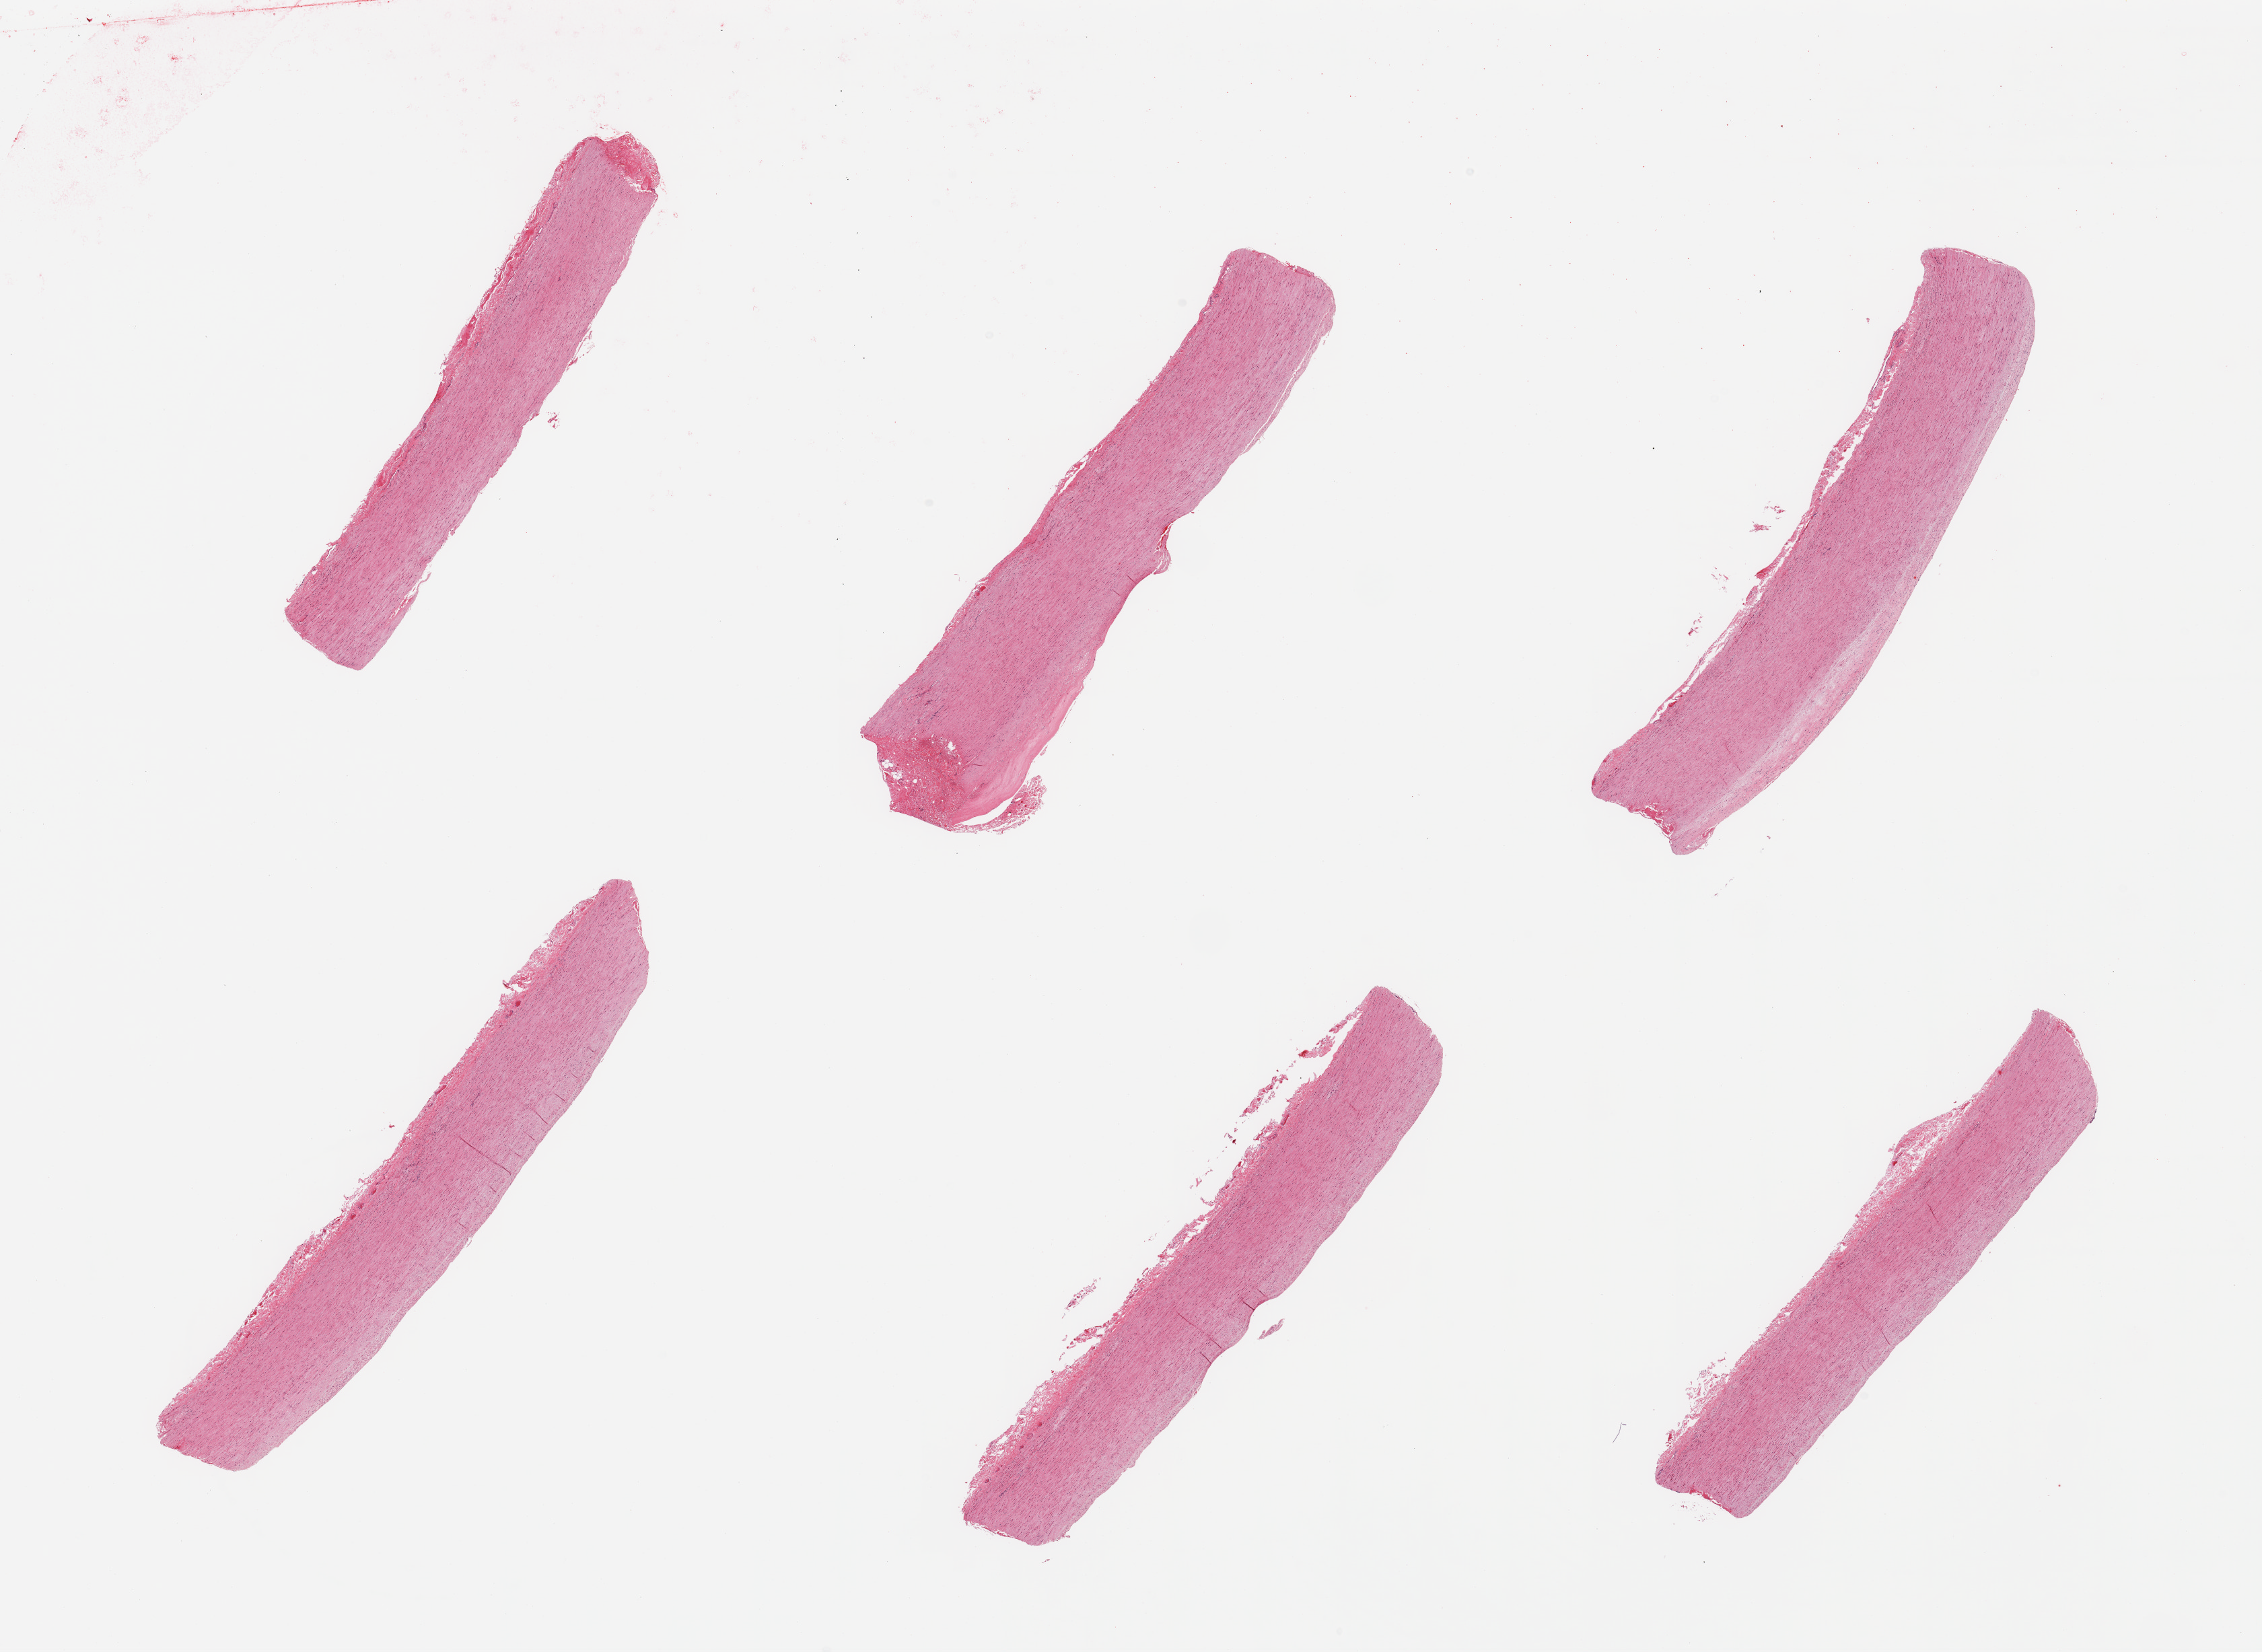
Hematoxylin and eosin (H&E) whole-slide image, brightfield, a low-resolution overview of the entire scanned area, about 26.6 x 19.4 mm, PAXgene-fixed paraffin-embedded (PFPE) section, target tissue: aorta, tissue donor sample. Donor sex: female.
Pathologist's review note for this sample: 6 pieces; well trimmed; mild flat plaques.